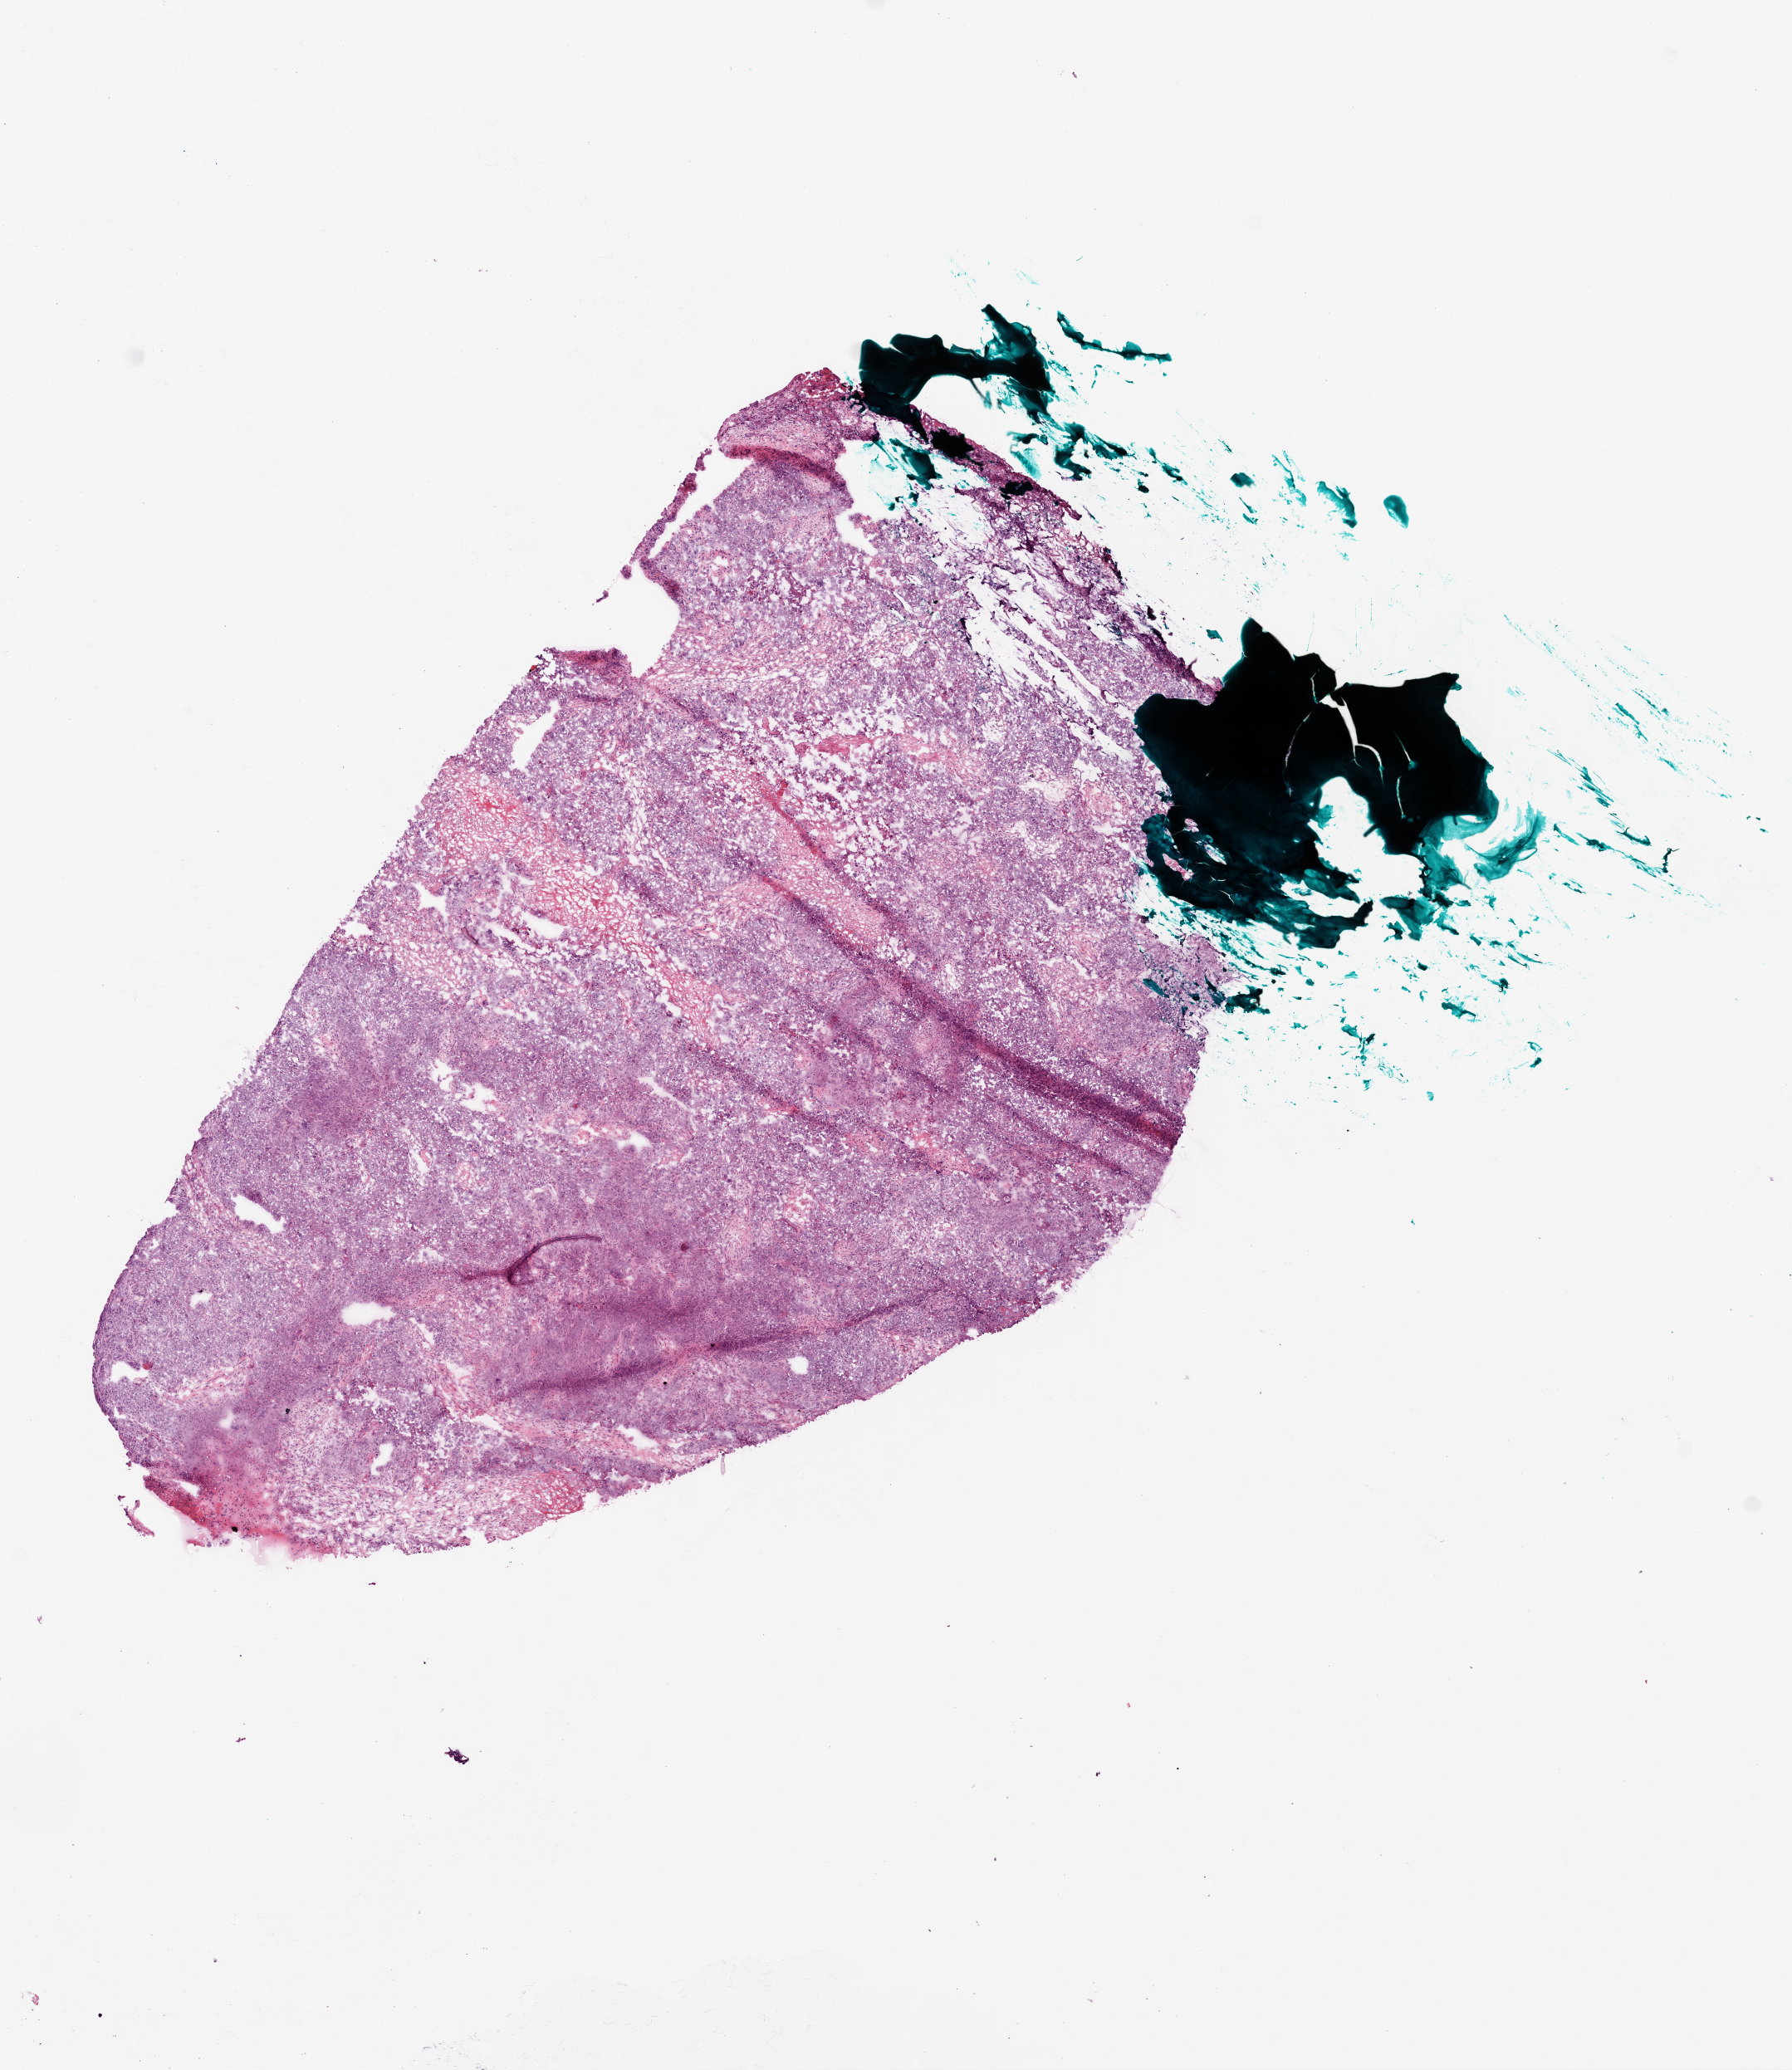
H&E-stained whole-slide image, shown as a low-resolution overview of the whole scanned area (about 8.7 x 10.1 mm, acquisition: 20x scan), frozen section from the bottom of the tissue portion, primary tumour sample from the ovary. Female, age 70 years at initial diagnosis. Histologic grade: G3 (poorly differentiated). Slide review estimates, as recorded: tumour cells 90%, tumour nuclei 95%, normal cells 5%, stromal cells 5%, necrosis 0%.
Pathologic diagnosis: Serous cystadenocarcinoma, NOS. FIGO stage: IIIC.